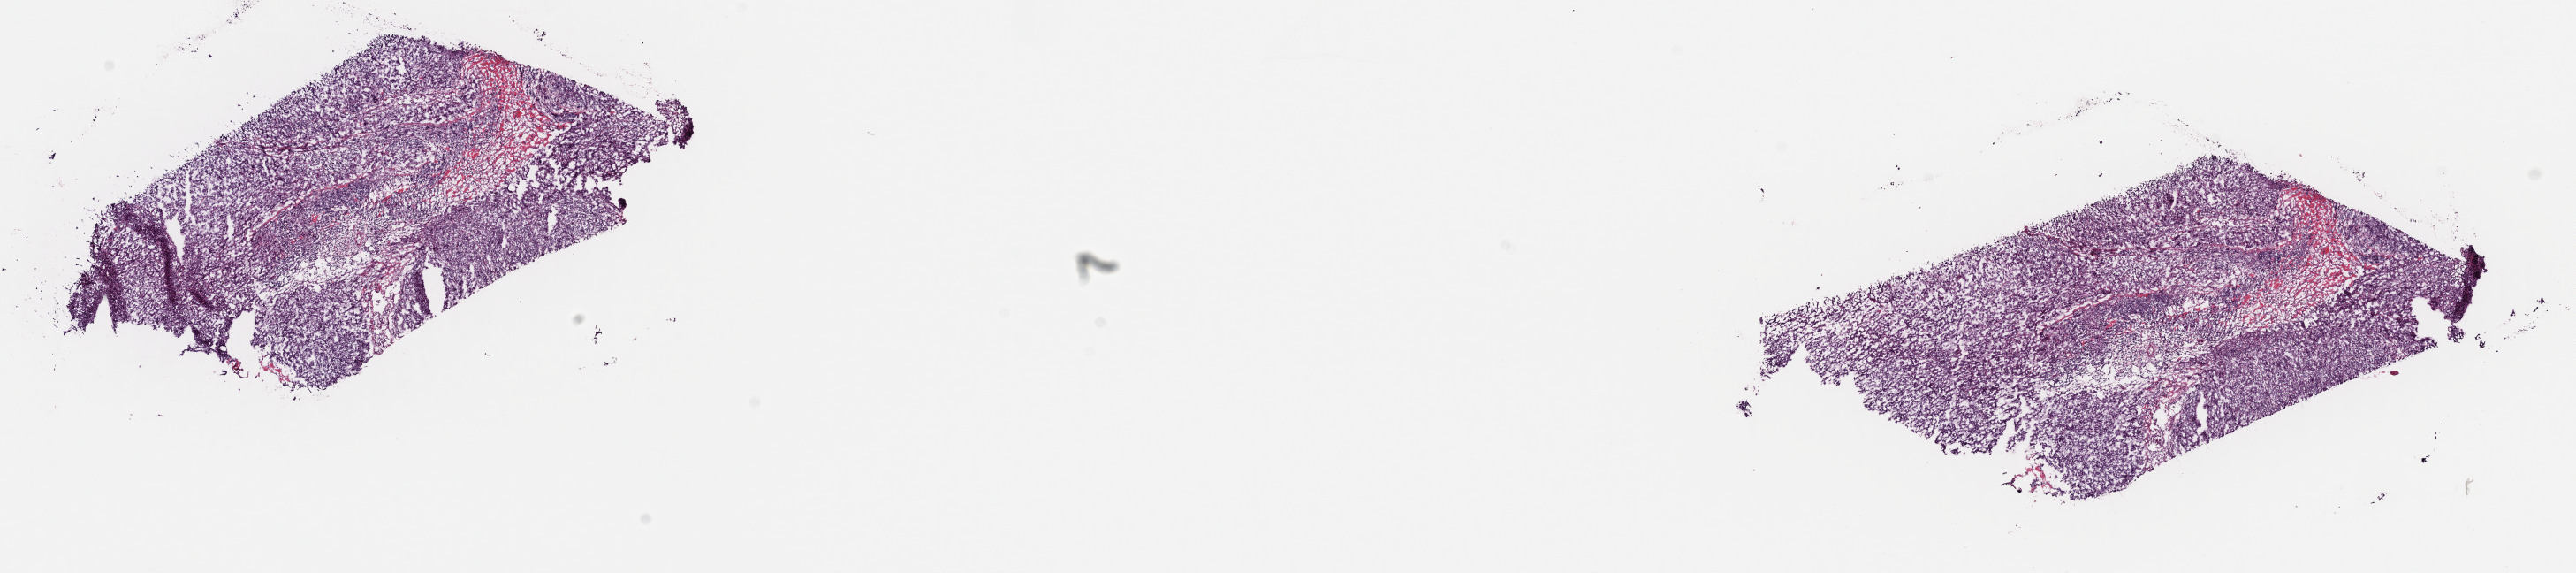
Digitized H&E tissue section (whole slide) — shown as a low-resolution overview of the whole scanned area (about 23.0 x 5.1 mm, from a 40x scan). Frozen section from the top of the tissue portion. Metastatic tumour sample. Female patient; age at initial diagnosis 42 years. Composition of this section per pathologist review: tumour cells 75%, tumour nuclei 75%, normal cells 0%, stromal cells 25%, necrosis 0%. Inflammatory infiltration, as recorded: lymphocyte infiltration 4%, monocyte infiltration 2%, neutrophil infiltration 0%.
This section: metastatic tumour tissue. Patient diagnosis: Malignant melanoma, NOS.